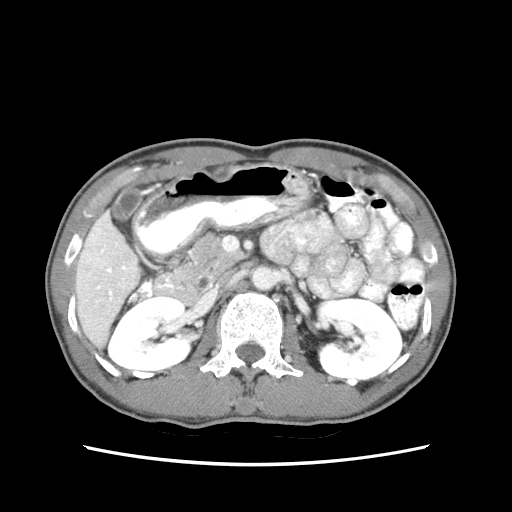
Contrast-enhanced abdominal CT (liver protocol), one axial slice; position 25 of 79 along the scan axis; reconstruction kernel STANDARD; 120 kVp; soft-tissue window (W 400 / L 40 HU); 2.5 mm slice thickness; 512 × 512 image matrix. From the clinical record (not read from this slice): diagnosis: hepatocellular carcinoma (patient treated with transarterial chemoembolisation; whether this scan precedes or follows treatment is not stated here); TNM stage (as recorded): Stage-IIIB; Child-Pugh class: A; tumour nodularity: multinodular.
Outlined on this slice (semi-automatically segmented with operator editing):
- liver parenchyma outside the tumour (the mass and vessels are separate outlines, so this box may not span the whole liver): bounding box (x1, y1, x2, y2) in pixels: (76, 212, 140, 344)
- liver vessels: (86, 219, 132, 303)